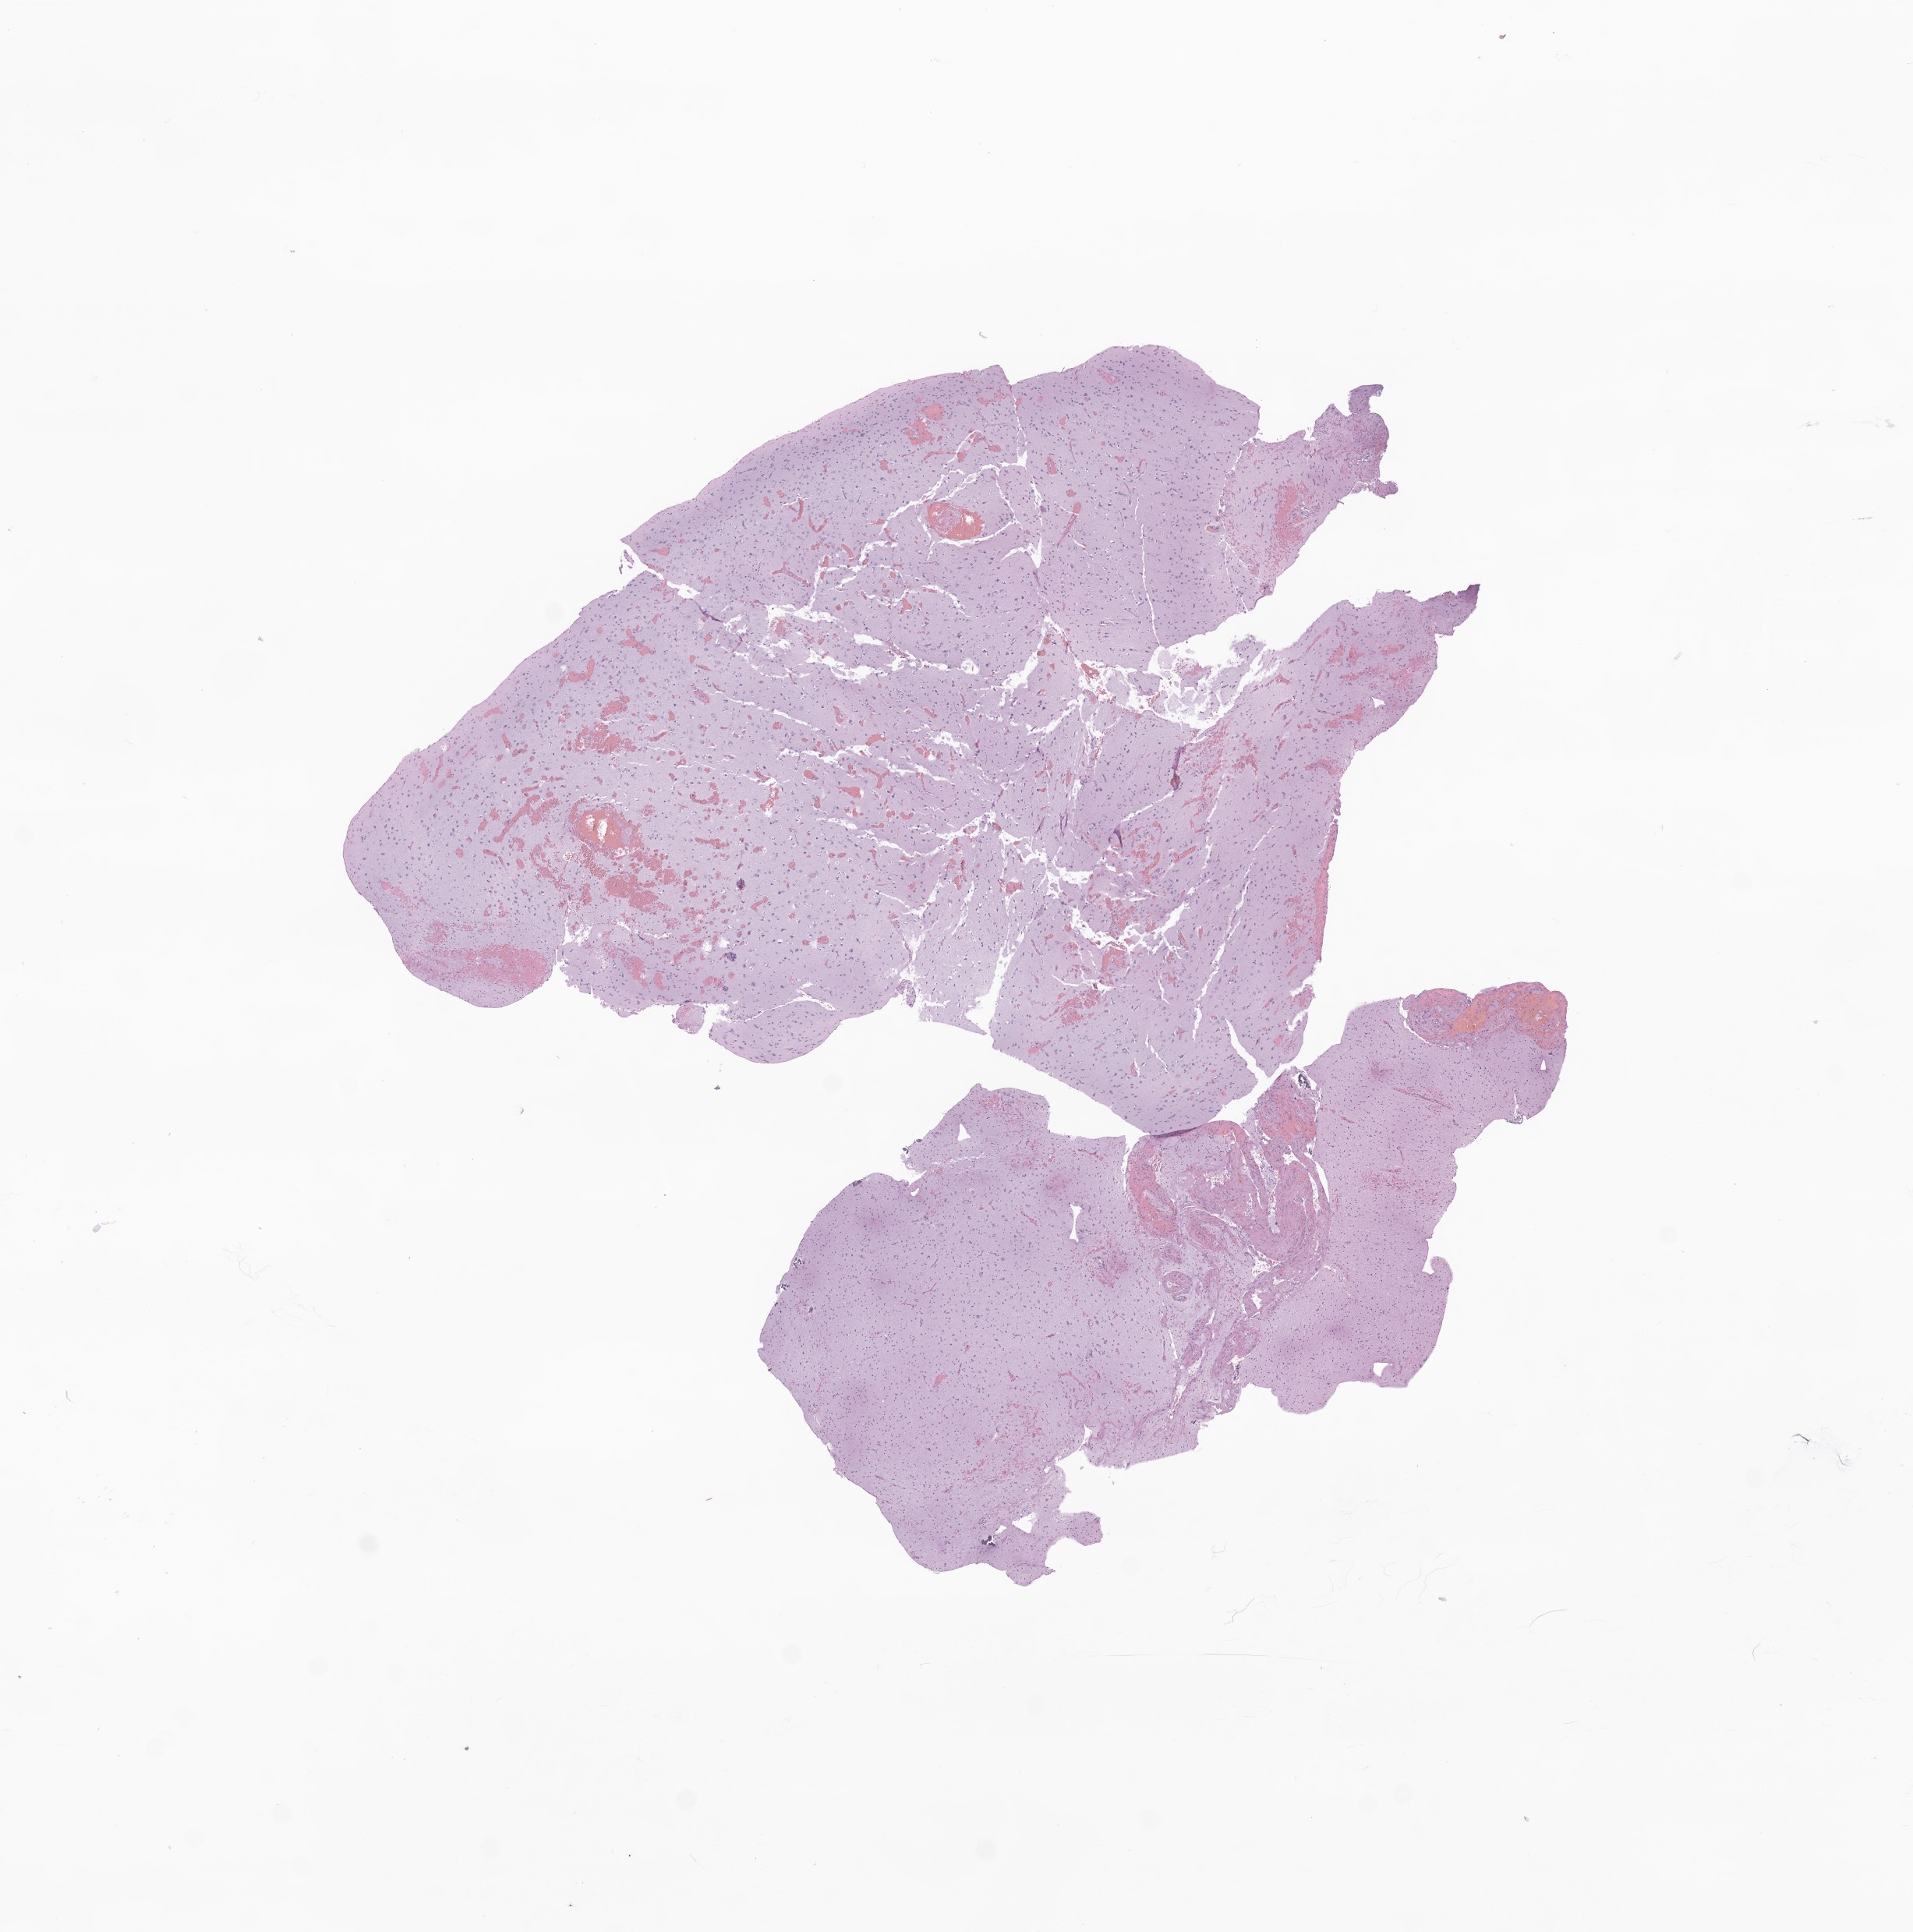
Whole-slide image, hematoxylin and eosin (H&E) stain of tumor tissue from the parietal lobe — whole scanned area (about 10.3 x 10.4 mm) shown as a low-resolution overview, FFPE section. Female patient, age 163 months (13 years 7 months).
Diagnosis: Astrocytoma, NOS.